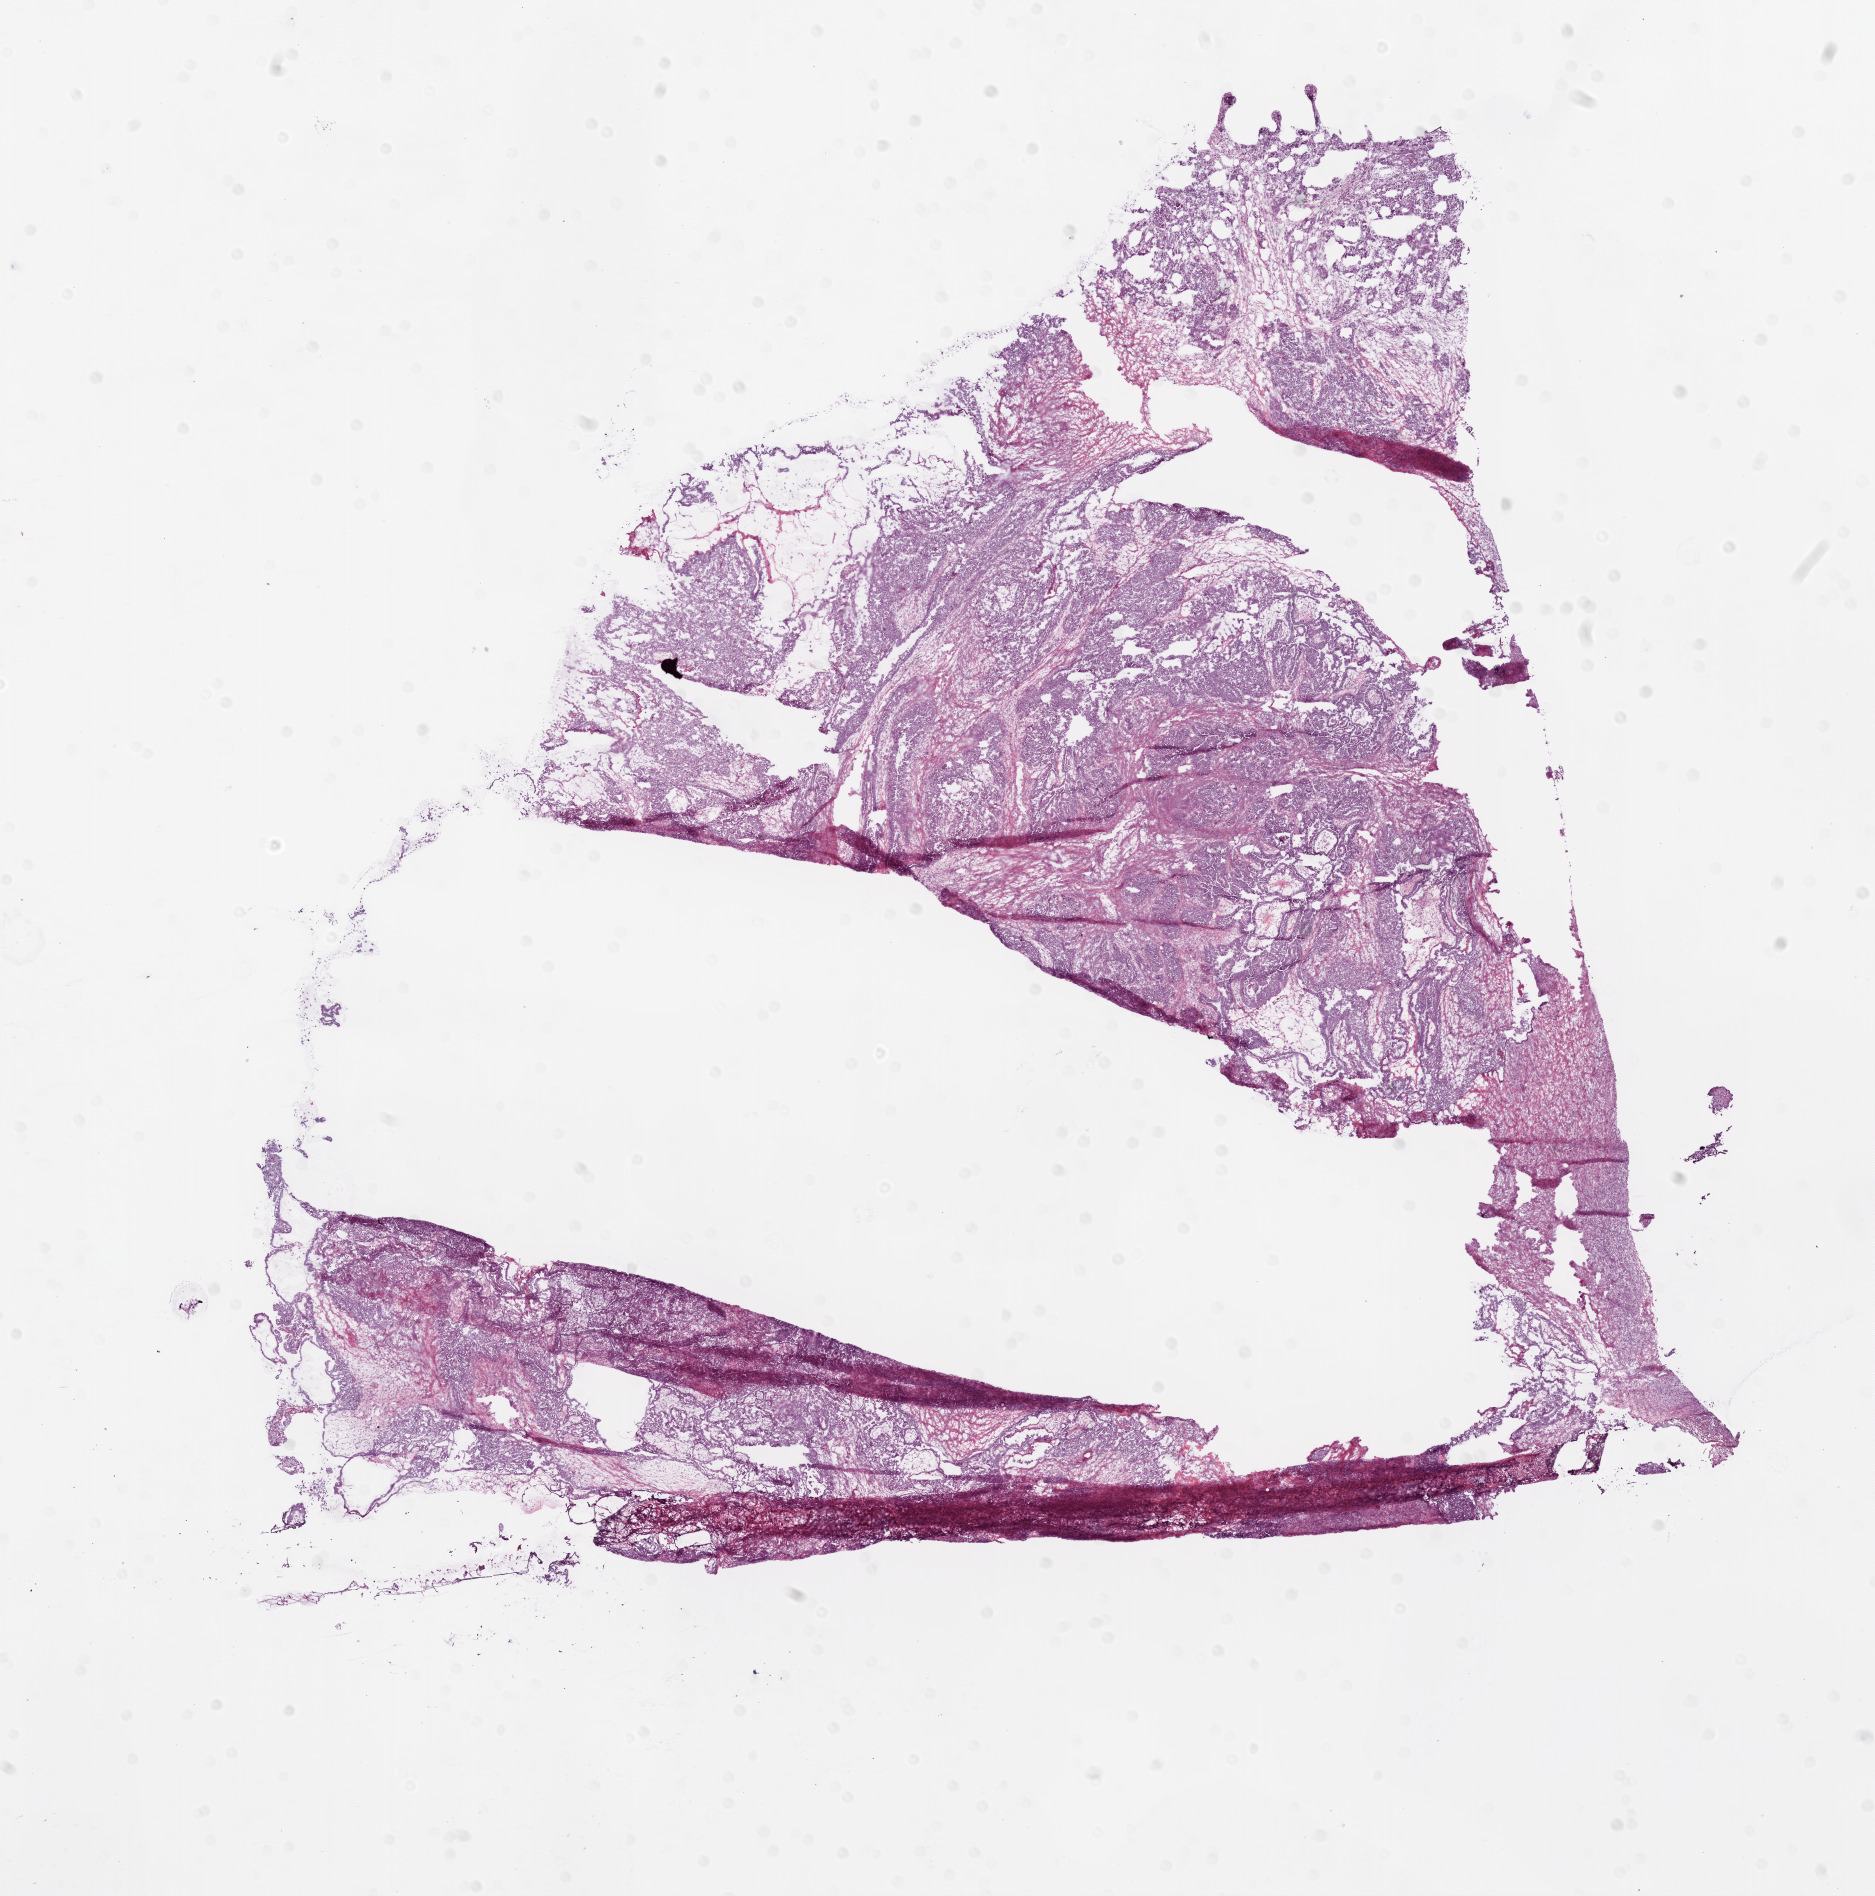
Hematoxylin and eosin (H&E) stained whole-slide image — shown as a low-resolution overview of the whole scanned area (about 15.0 x 15.2 mm, acquisition: 20x scan); frozen section from the top of the tissue portion; primary tumour sample from the ovary. Female patient; age at initial diagnosis 65 years. Histologic grade: G3 (poorly differentiated). Composition of this section per pathologist review: tumour cells 80%, tumour nuclei 80%, normal cells 0%, stromal cells 20%, necrosis 0%.
Laterality: bilateral. Histologic diagnosis: Serous cystadenocarcinoma, NOS. FIGO stage: IV.